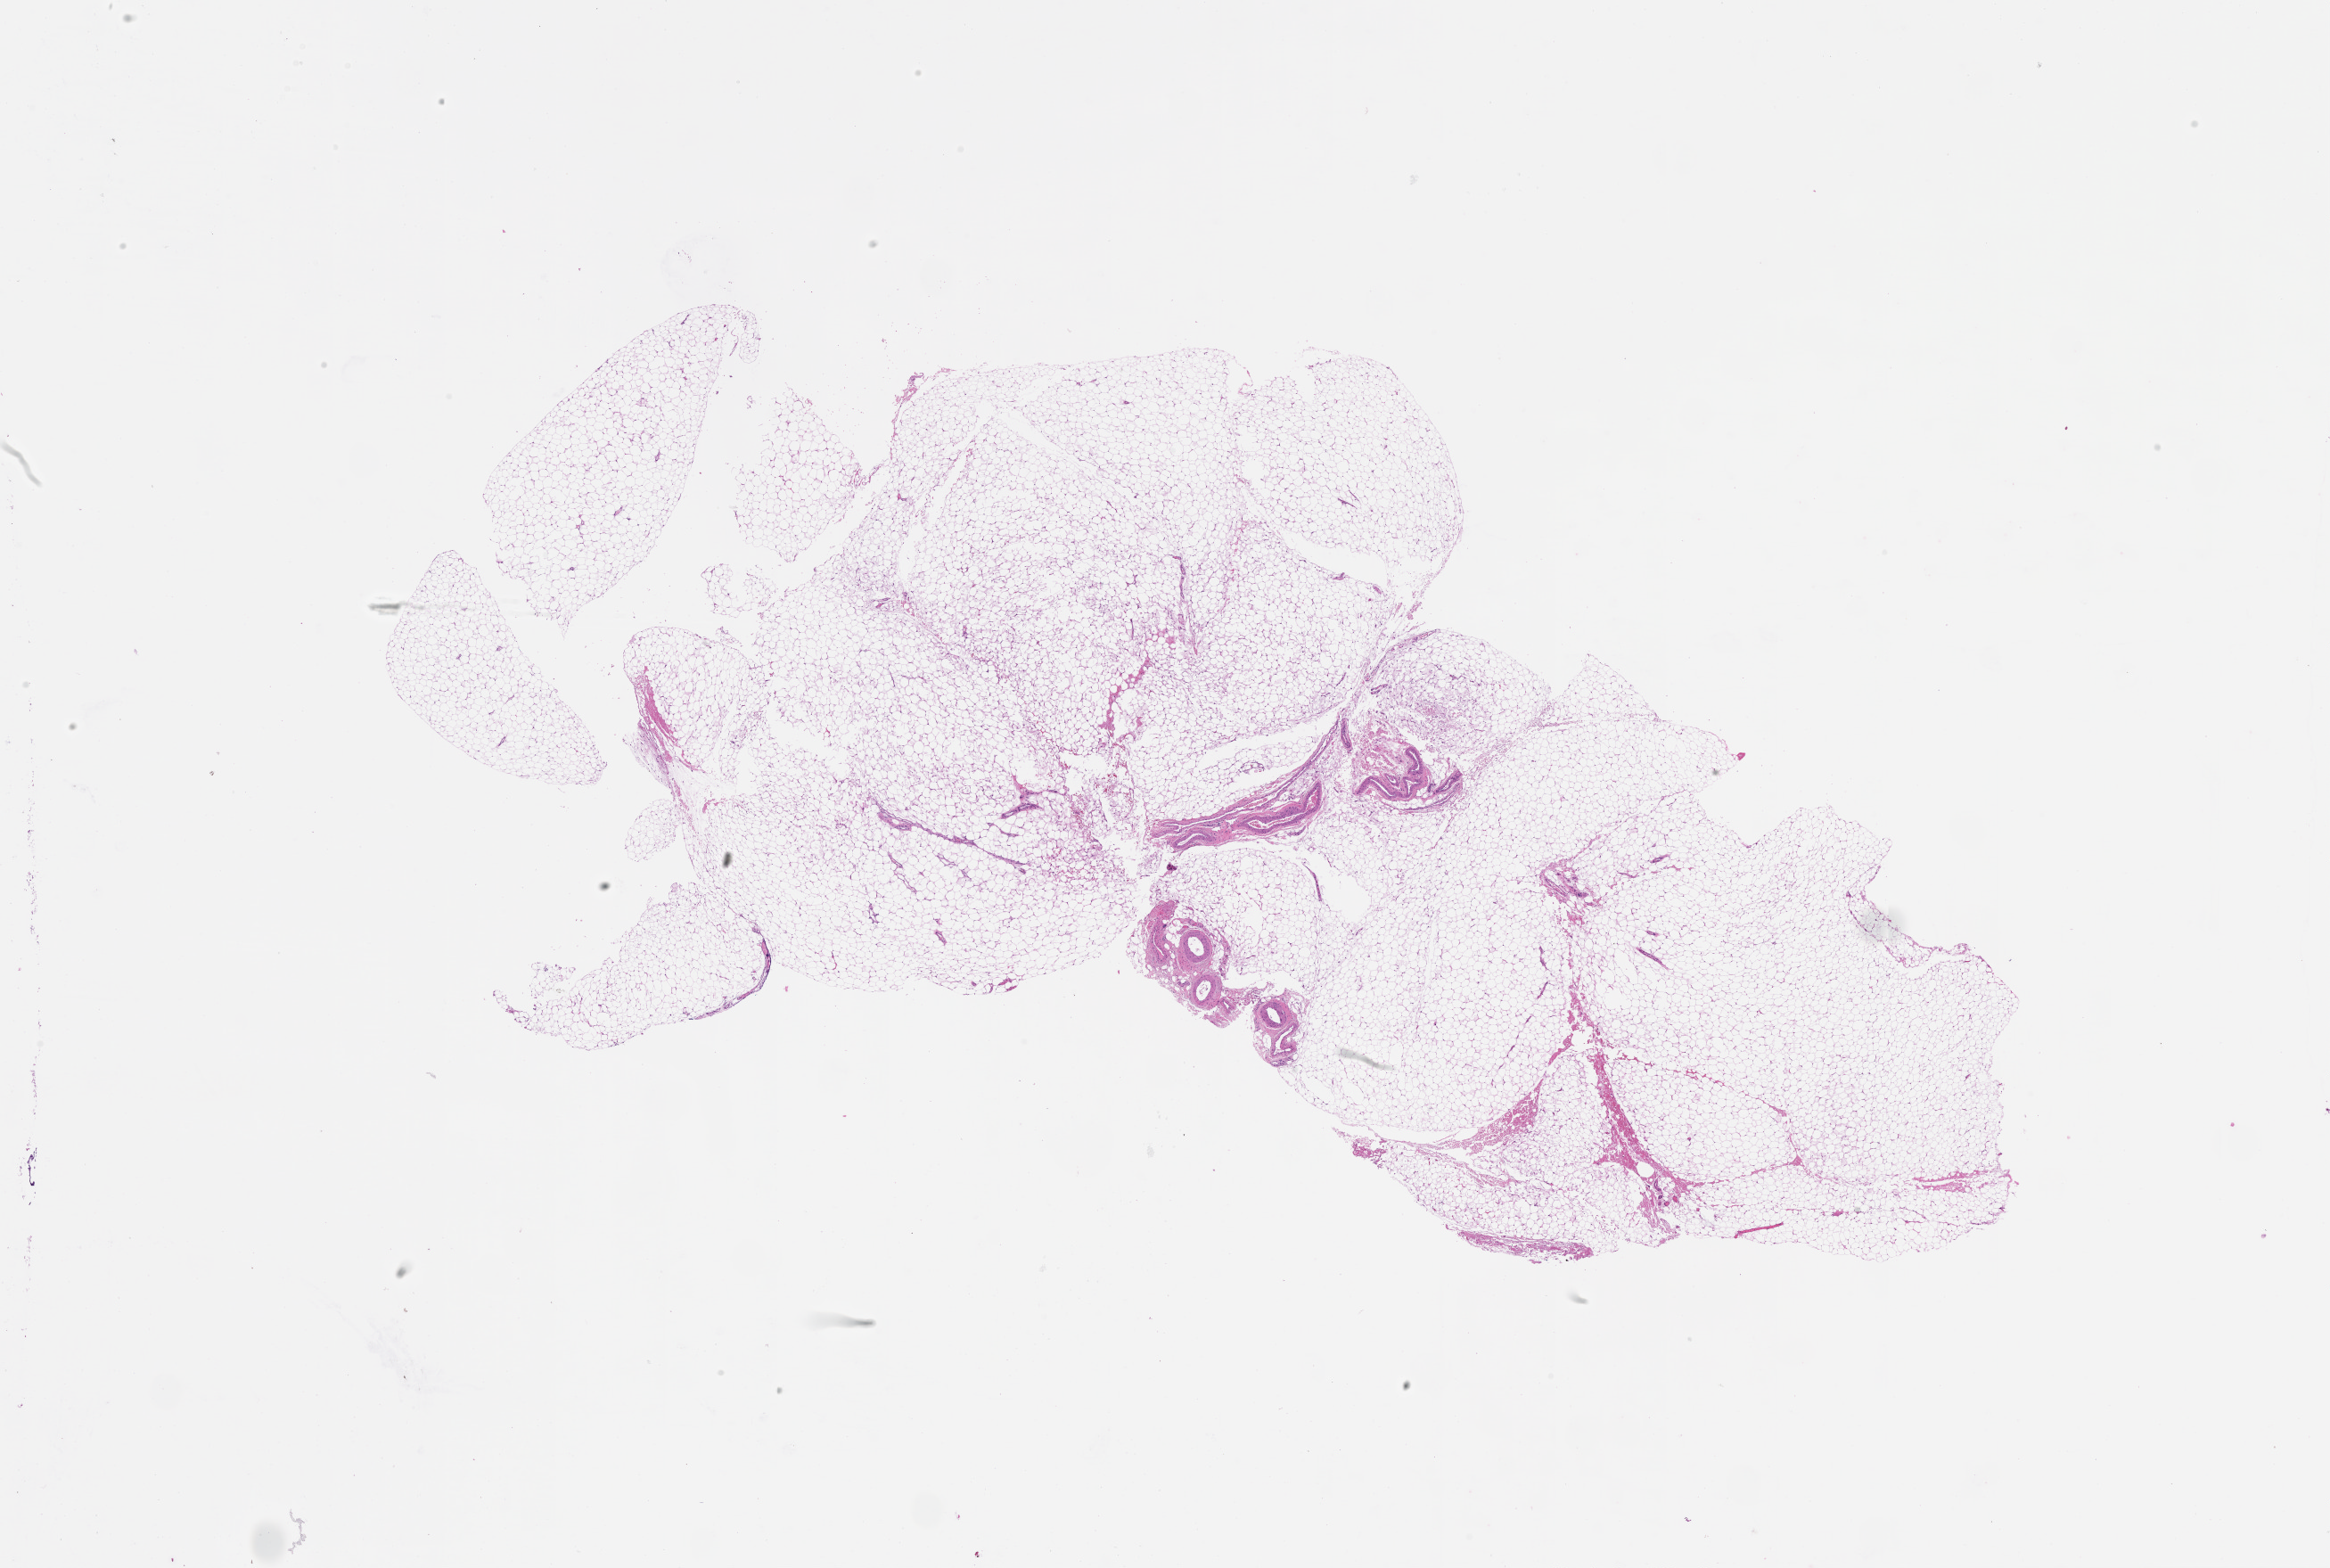
Digitized H&E tissue section (whole slide), low-resolution overview of the scanned area, about 21.0 x 14.2 mm.
Patient diagnosis (cohort enrolment): sarcoma (site not recorded at cohort level).